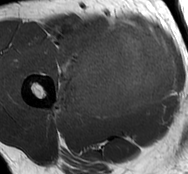
MRI of an extremity soft-tissue mass, one axial slice. Position 38 of 93 along the scan axis. MR volume resampled by the dataset authors to the PET/CT grid (not the native acquisition matrix). 3.27 mm slice thickness. 188 × 174 image matrix, field of view 184 × 170 mm. Male patient. Case-level facts recorded for this patient, not image findings: histological type: undifferentiated - pleiomorphic; grade: high; site of the primary tumour: right thigh.
Outlined on this slice (expert contour drawn on MRI and transferred to this co-registered scan by the dataset authors):
- gross tumour volume including surrounding oedema: box from (x=54, y=21) to (x=178, y=120) px
- gross tumour volume (mass): (x=72, y=23)–(x=176, y=118)